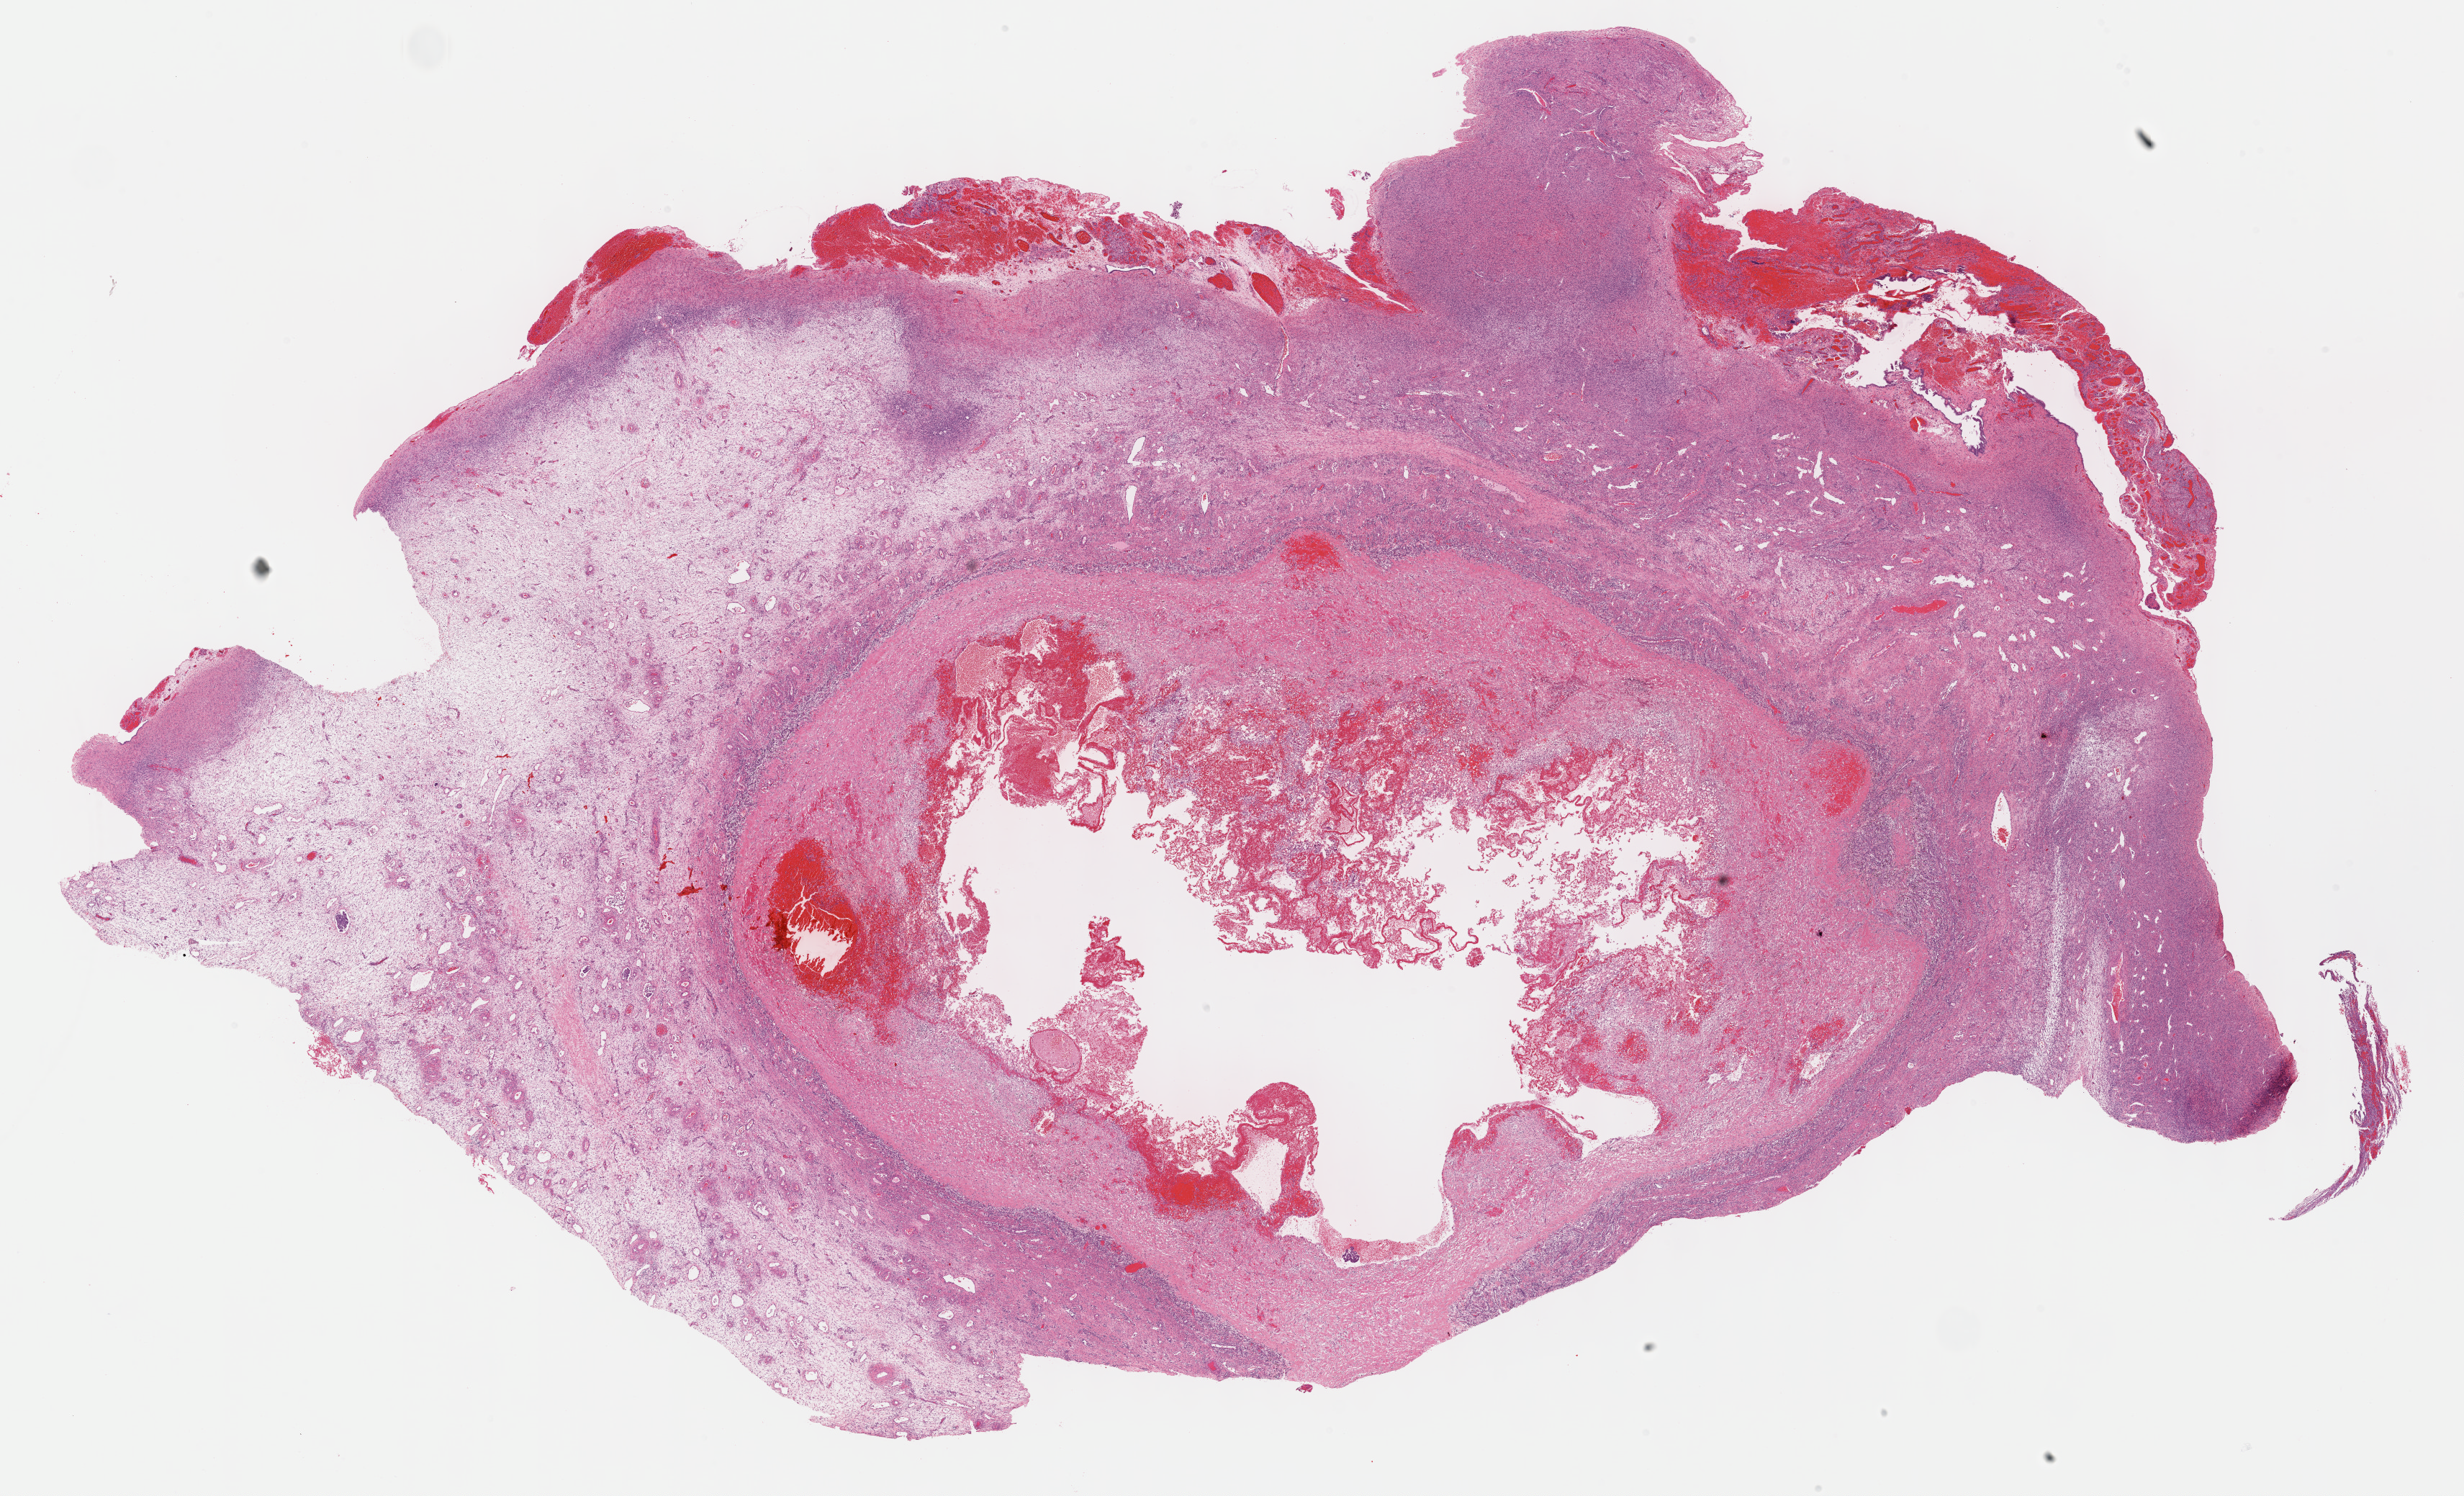
Hematoxylin and eosin (H&E) stained whole-slide image, shown as a low-resolution overview of the whole scanned area (about 27.7 x 16.8 mm), formalin-fixed paraffin-embedded (FFPE) diagnostic section, ovary, primary tumour sample. Female, age 45 years at initial diagnosis. Histologic grade: G3 (poorly differentiated).
FIGO stage: IIIC. Pathologic diagnosis: Serous cystadenocarcinoma, NOS.